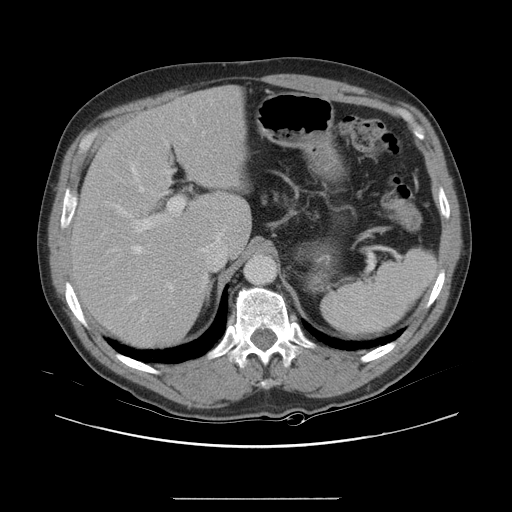
Contrast-enhanced abdominal CT, one axial slice. Intravenous contrast given. Soft-tissue window (W 400 / L 40 HU). 5 mm slice thickness. 512 × 512 image matrix, field of view 408 × 408 mm. Male patient, age 64 years. From the clinical record (not read from this slice): diagnosis: colorectal cancer liver metastases, imaged before liver resection; multiple liver metastases: yes; largest metastasis: 3.2 cm.
Outlined on this slice (outlined manually by an expert reader):
- hepatic veins: bounding box [x1, y1, x2, y2] px = [129, 167, 223, 302]
- liver: [74, 89, 251, 345]
- planned liver remnant (the part of the liver to remain after resection): [88, 89, 251, 249]
- portal vein (with intrahepatic branches): [118, 171, 184, 290]